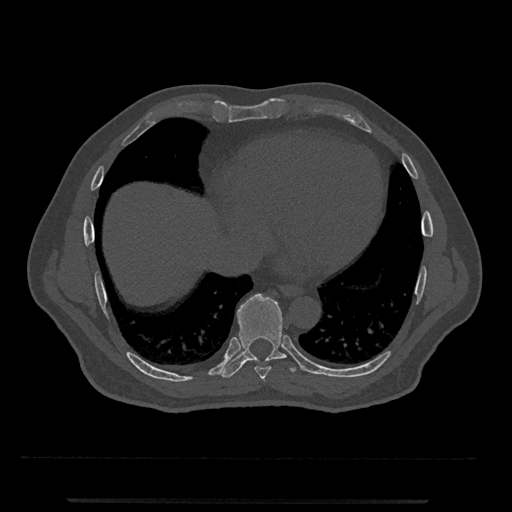
CT including the spine, one axial slice; slice 594 of 797 in the series (ordered by position); reconstruction kernel Br40s/3; bone window (W 1800 / L 400 HU); 512 × 512 image matrix, field of view 419 × 419 mm. Patient: male, 63 years. From the clinical record (not read from this slice): primary cancer: prostate.
Structures marked on this image (semi-automatically segmented with operator editing):
- T7 vertebra: box from (x=263, y=378) to (x=265, y=380) px
- T8 vertebra: (x=254, y=362)–(x=271, y=380)
- T9 vertebra: (x=221, y=293)–(x=298, y=378)